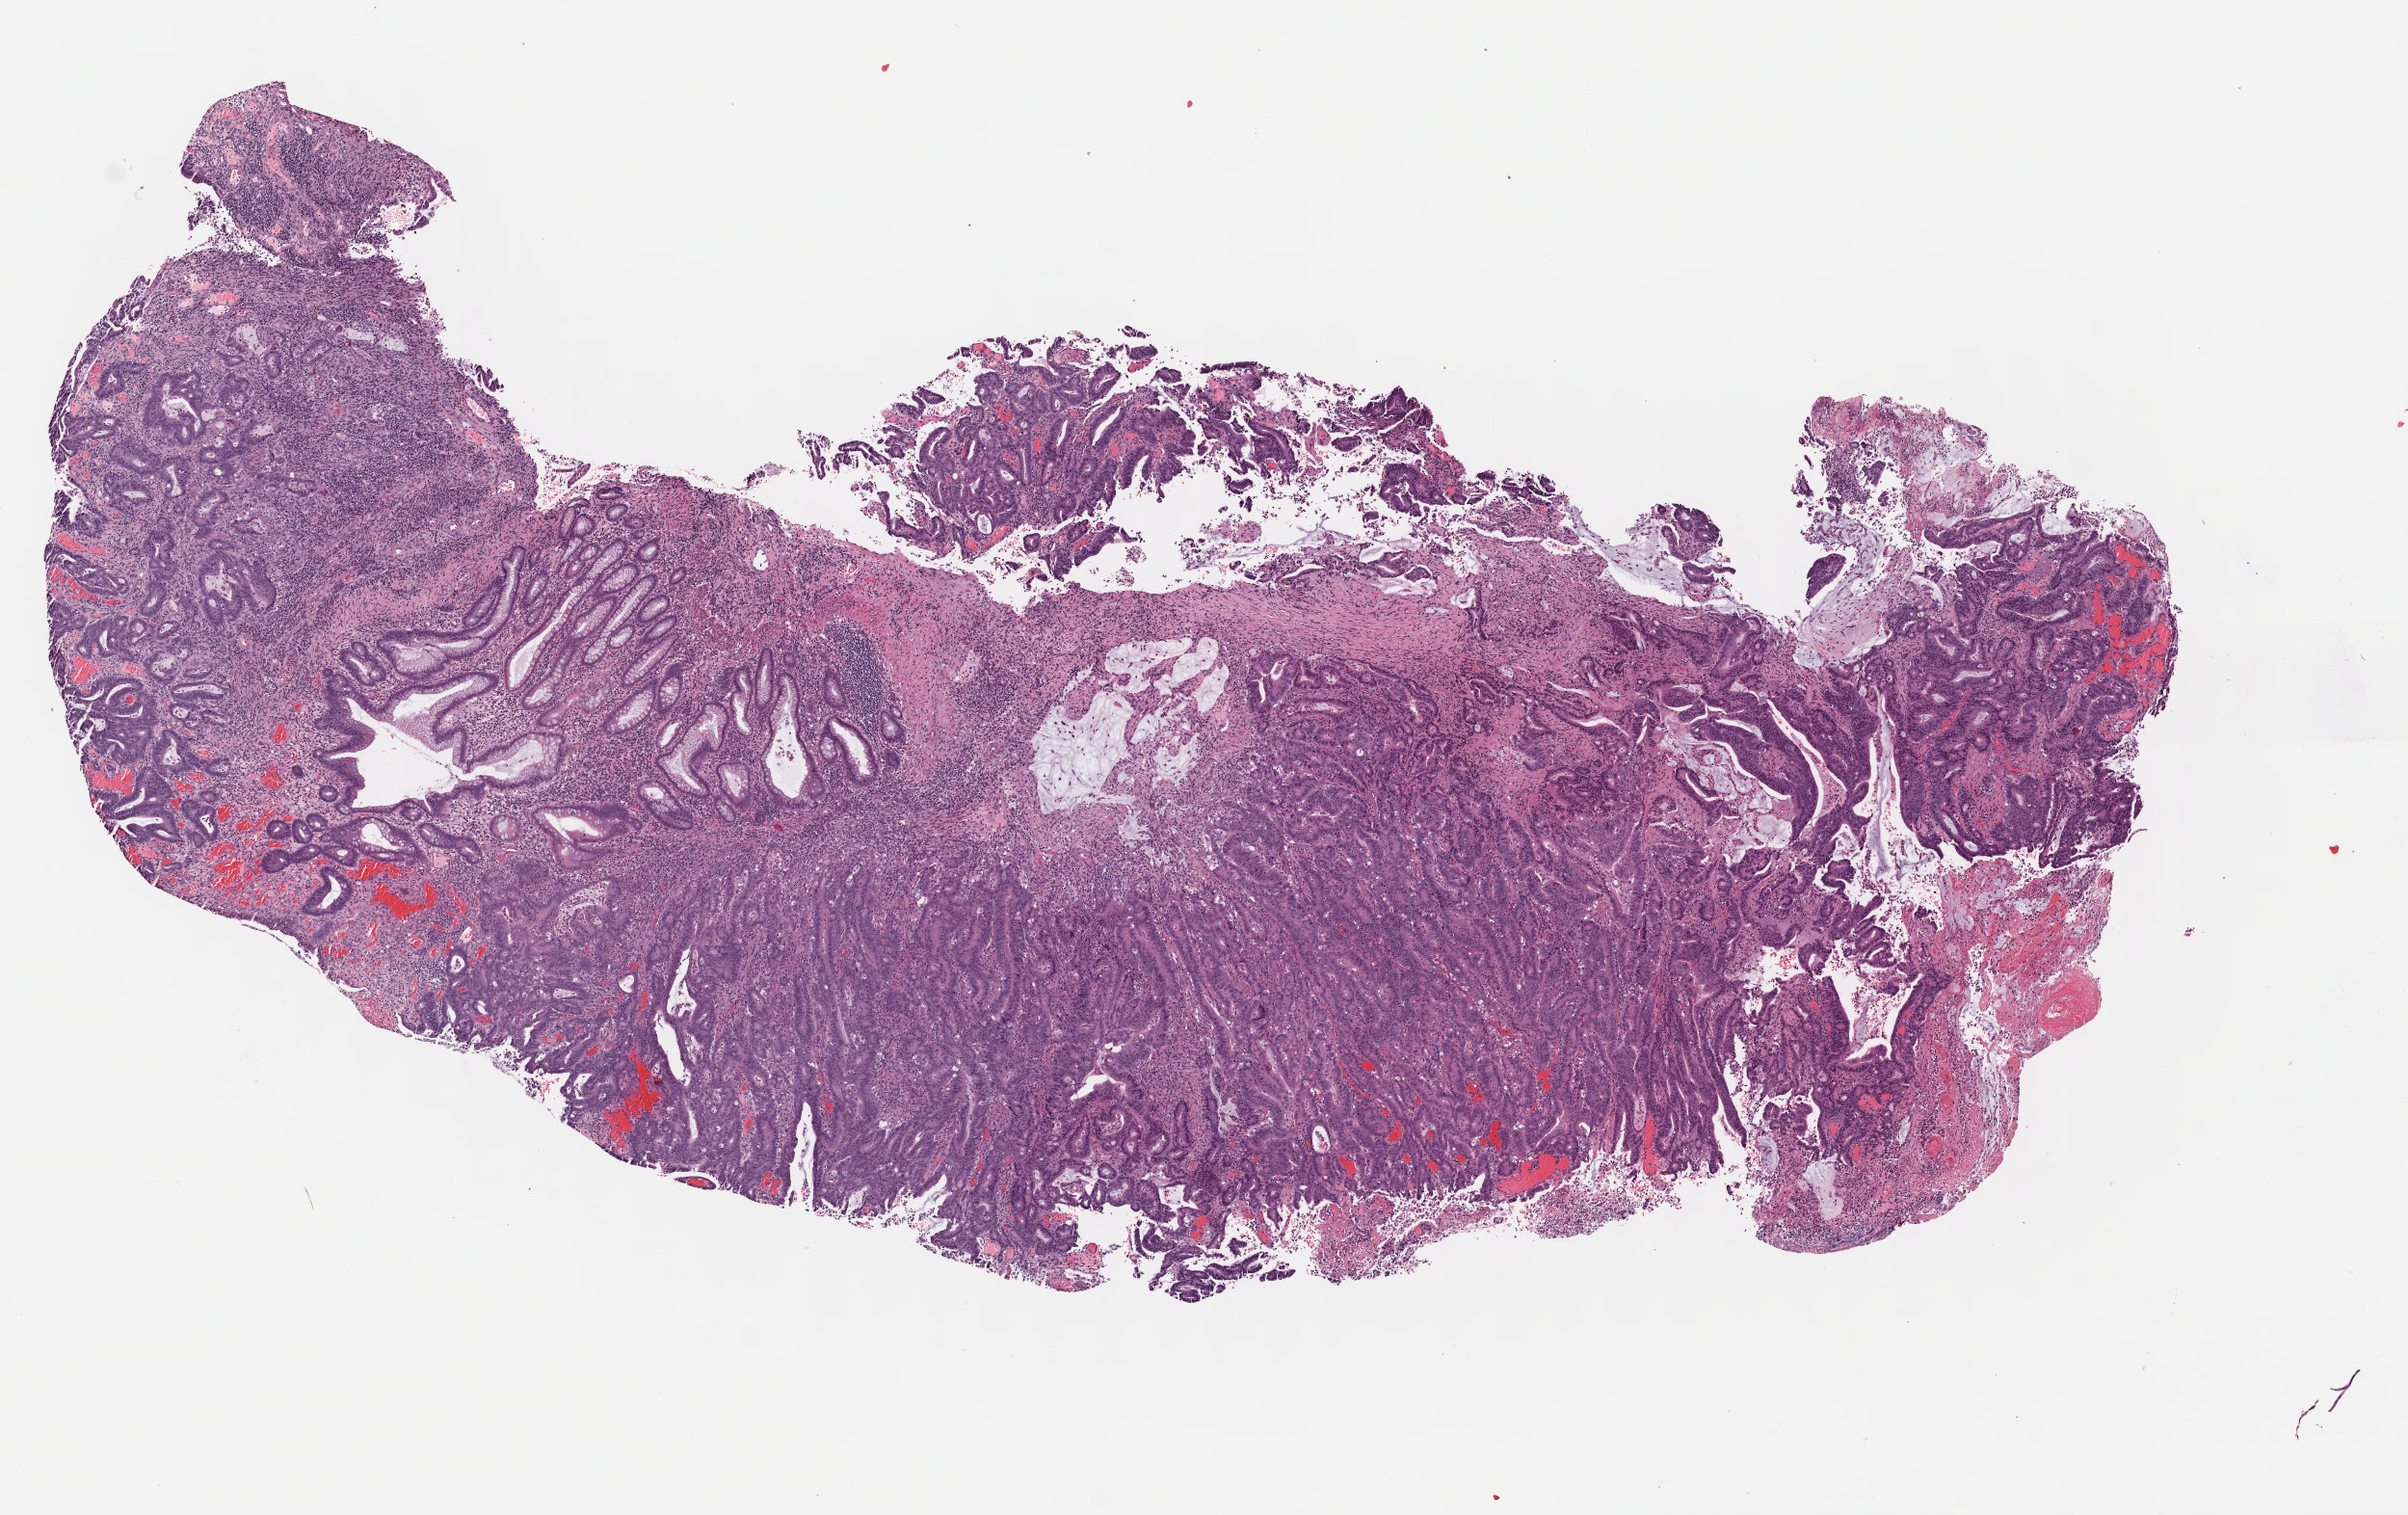
H&E-stained whole-slide image — a low-resolution overview of the entire scanned area, about 9.8 x 6.2 mm (slide scanned at 40x); frozen section from the bottom of the tissue portion; sample: primary tumour, colon. Patient: female, age at initial diagnosis 71 years.
Diagnosis: Mucinous adenocarcinoma.